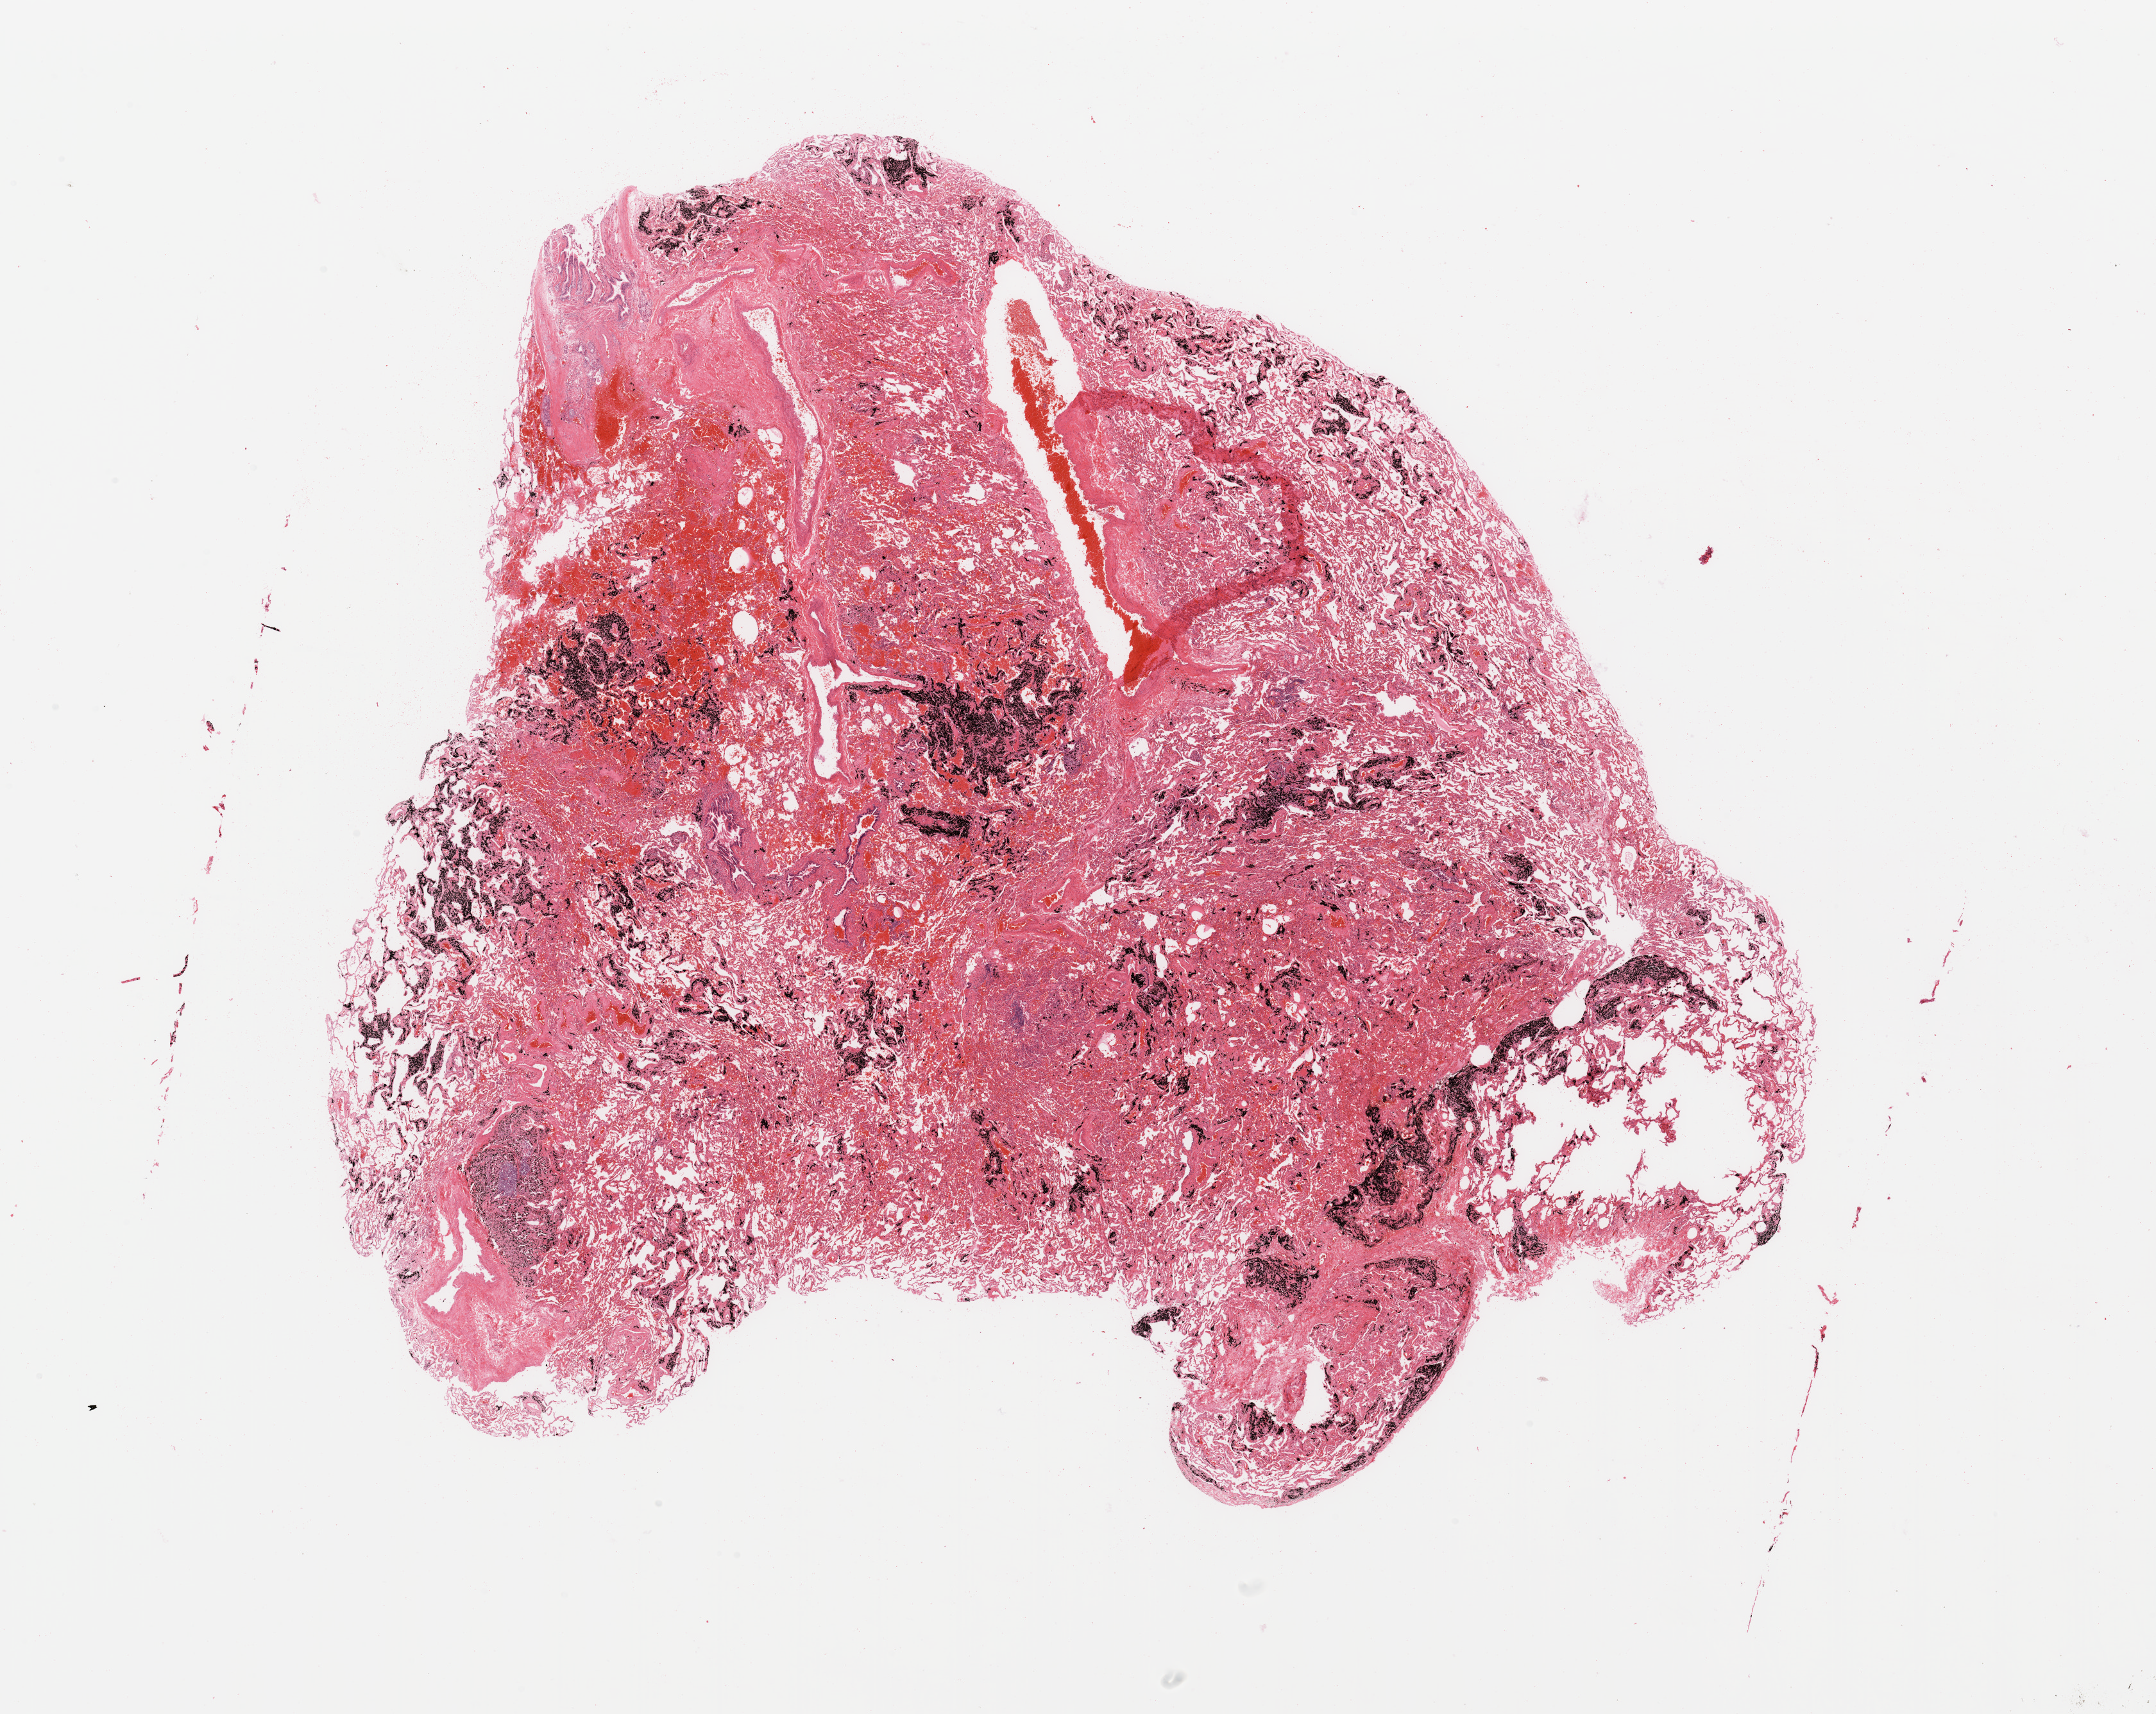
Hematoxylin and eosin (H&E) stained whole-slide image, a low-resolution overview of the entire scanned area, about 26.6 x 21.1 mm; normal (non-tumour) tissue sample, sampled site: lung. Patient: male, age 65 years.
This section: normal (non-tumour) tissue from the same patient. Patient diagnosis: Adenocarcinoma, NOS.